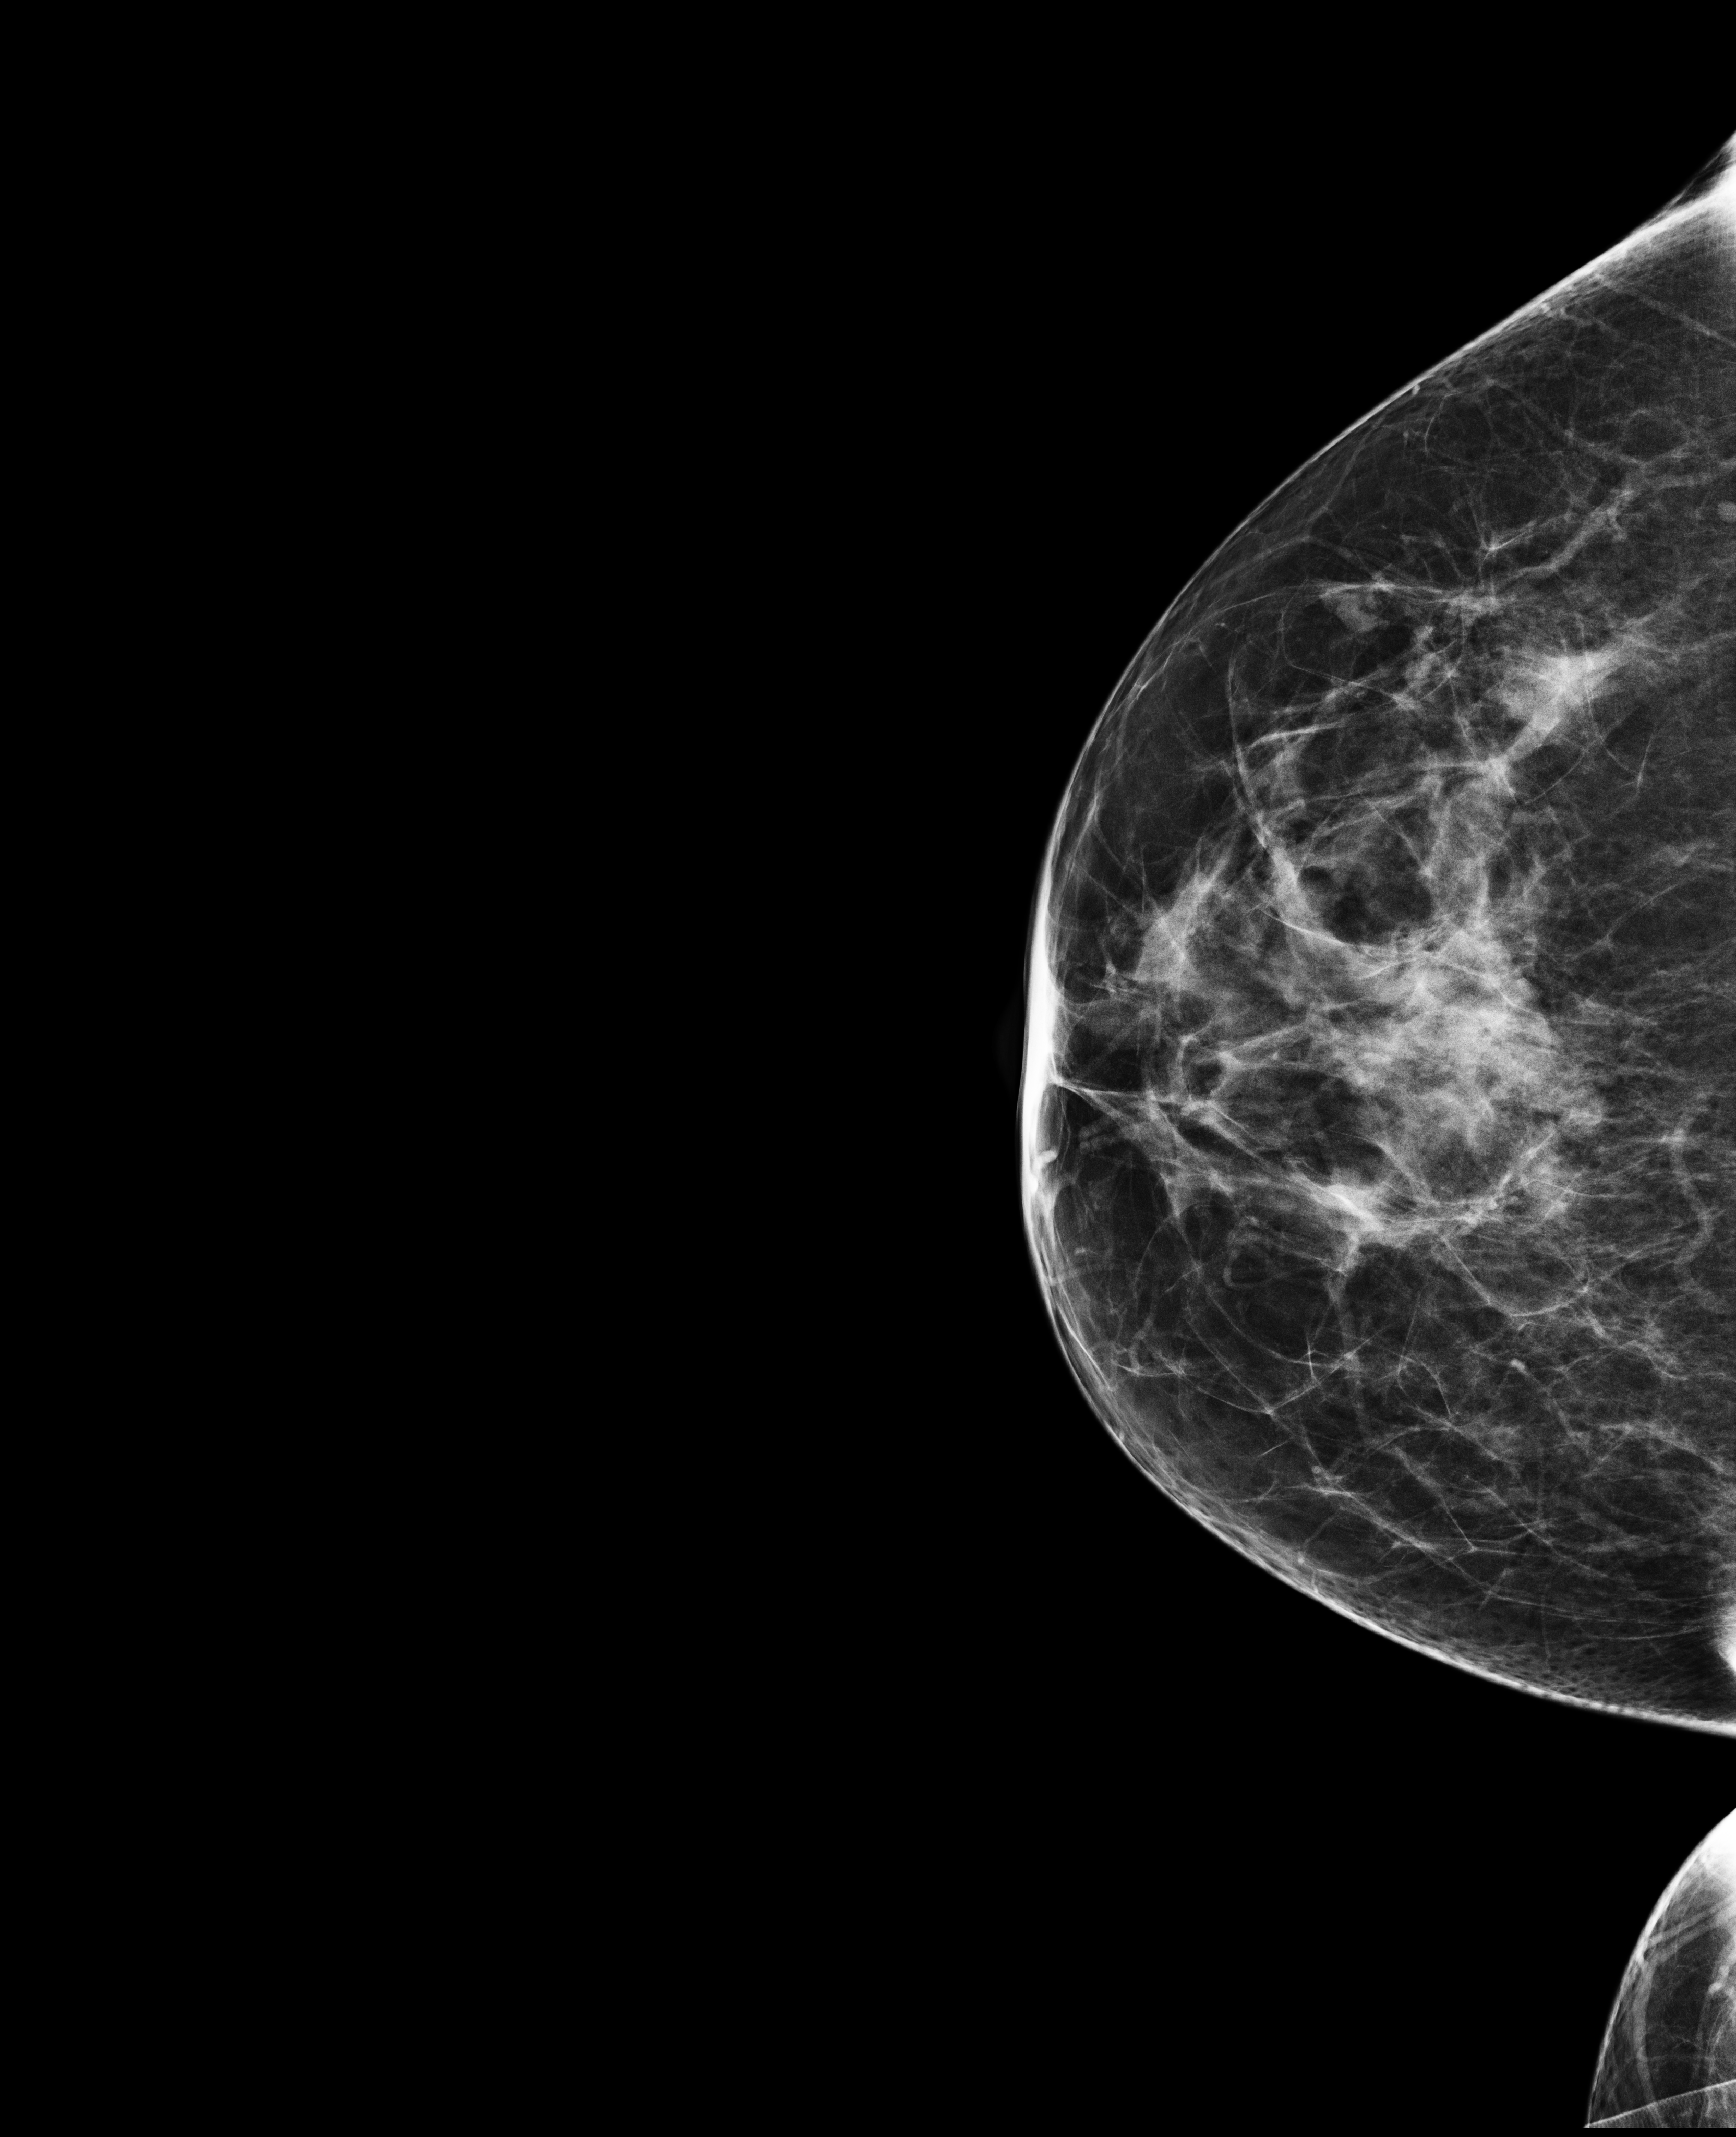
Full-field digital mammogram (FFDM), right breast, cranio-caudal projection, annual screening mammography examination, system: Selenia Dimensions. Patient: female, 44 years.
Breast density at the screening exam (both breasts): heterogeneously dense (BI-RADS density category c). Final BI-RADS assessment for this screening round (tomosynthesis exam, both breasts): category 2. Recall: recalled for additional imaging after this screen.